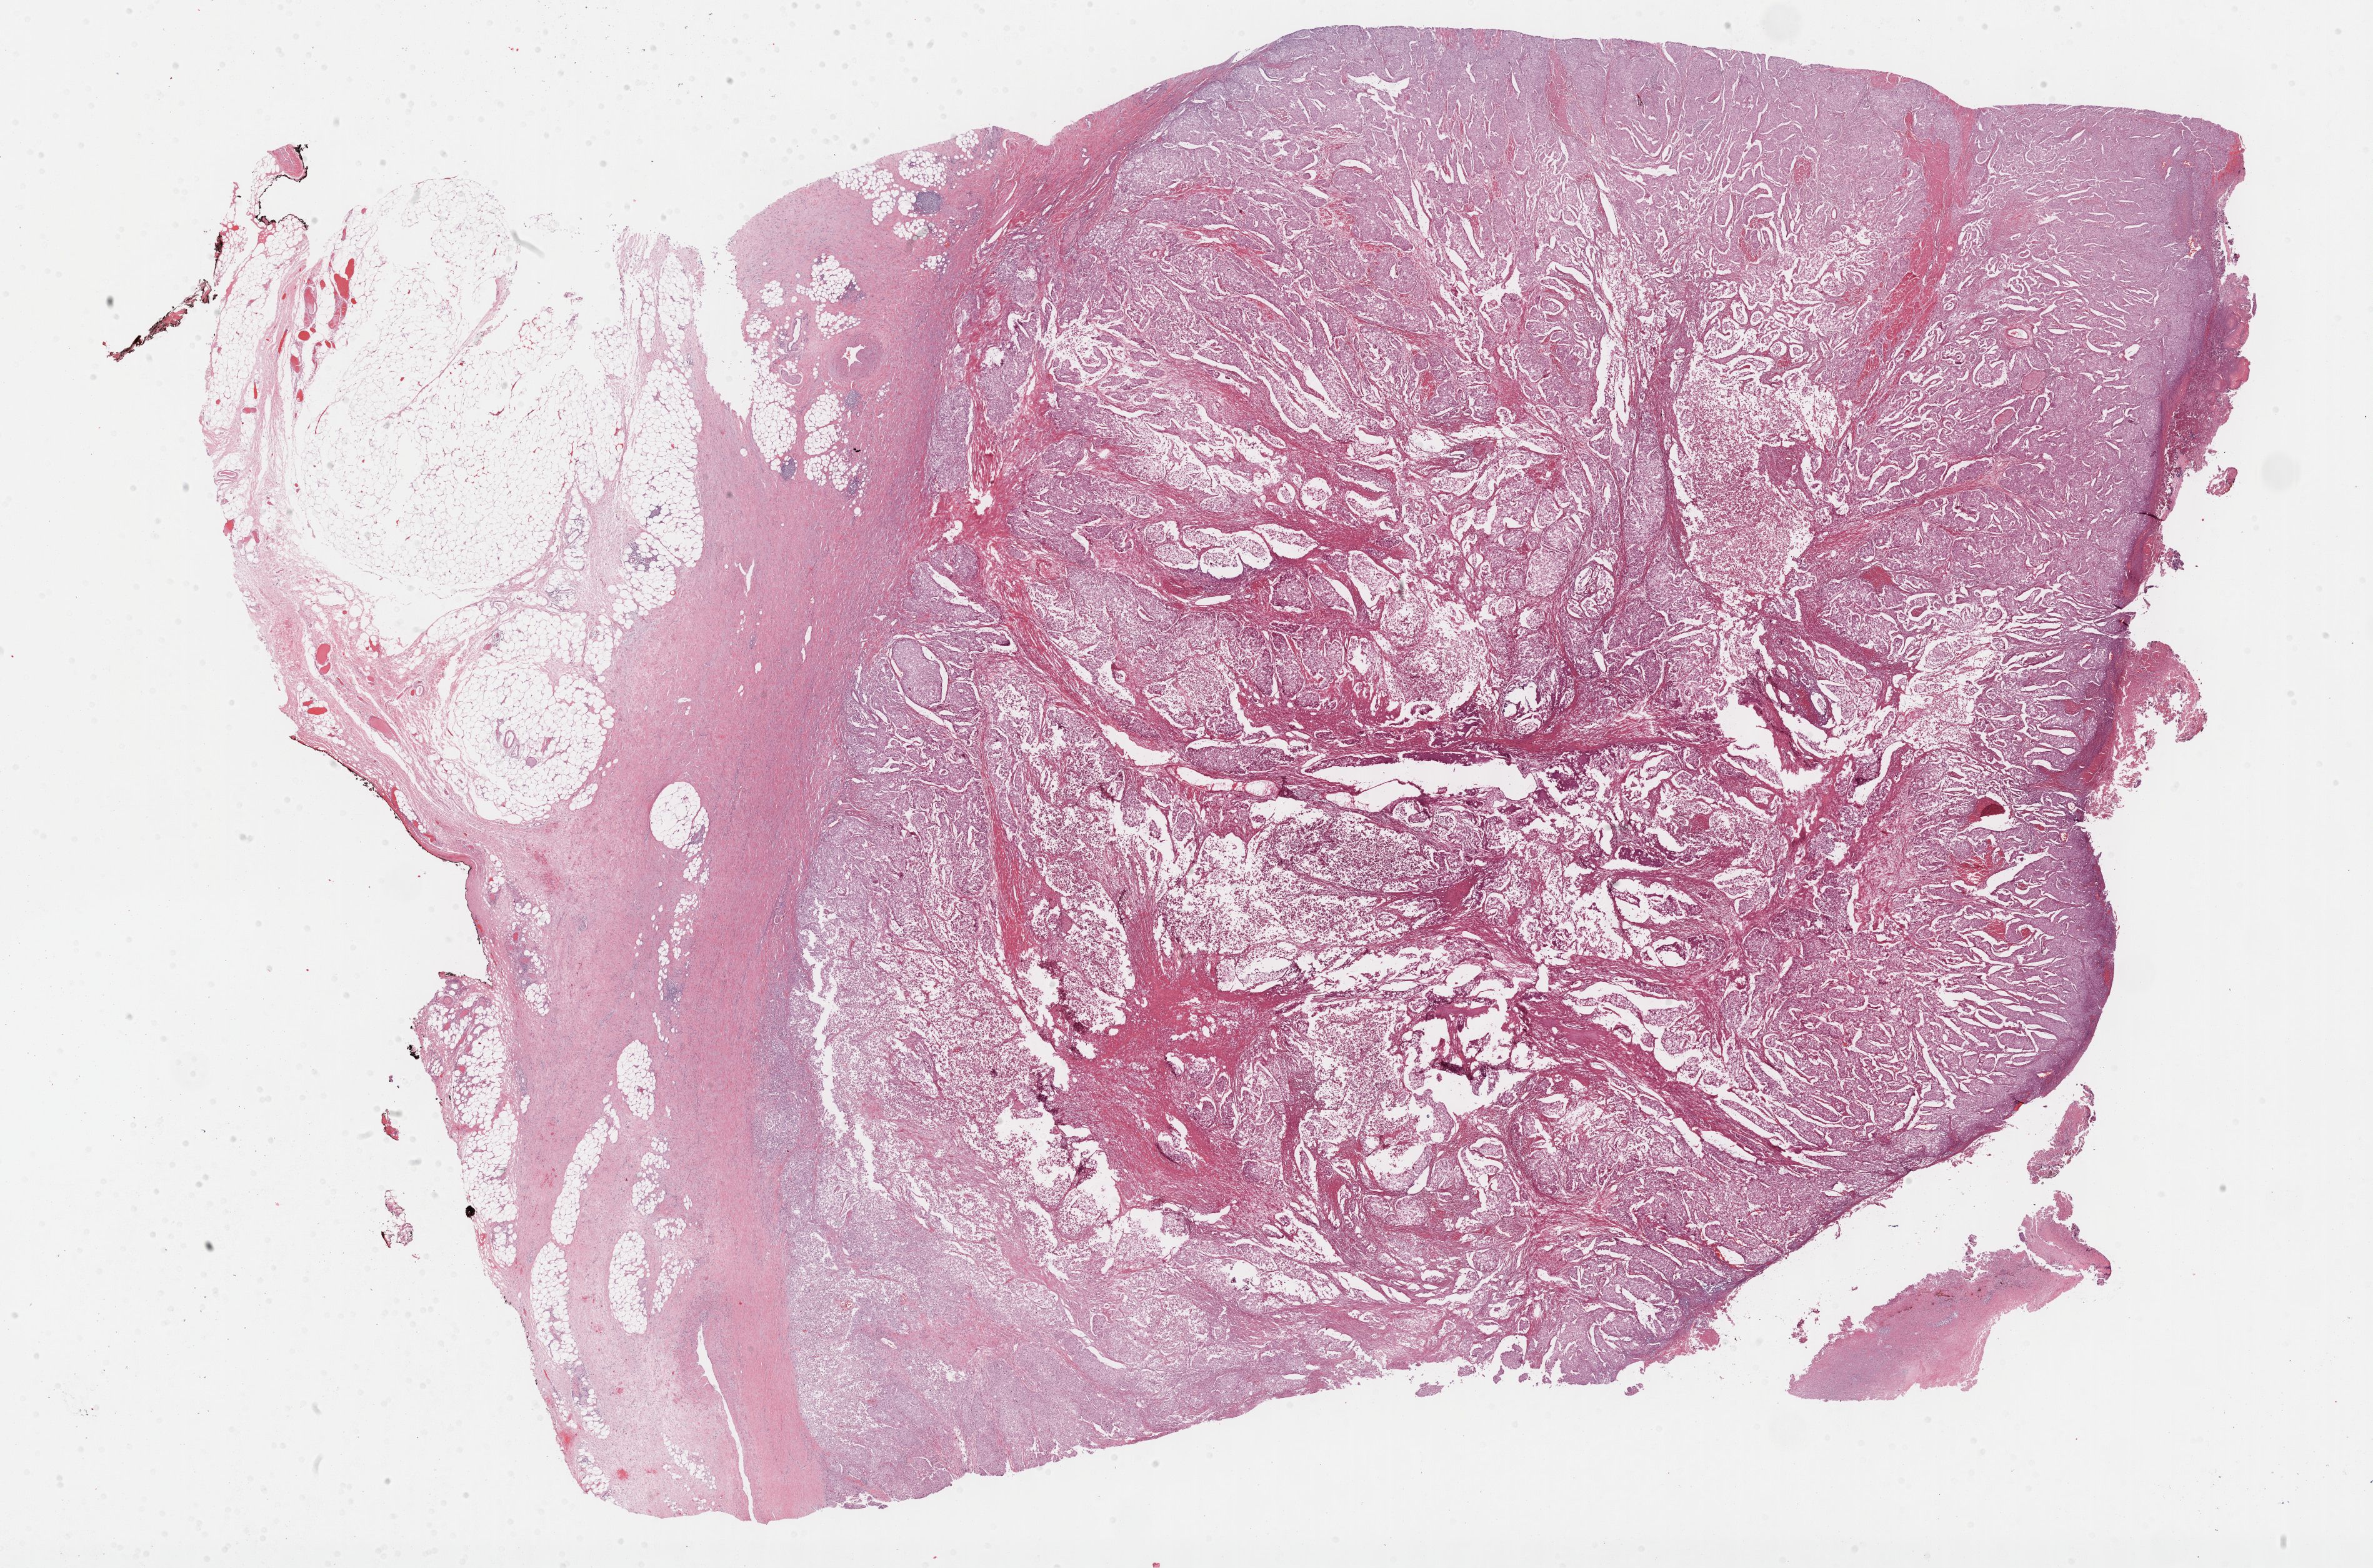
Digitized H&E-stained tissue section (whole slide) — shown as a low-resolution overview of the whole scanned area (about 30.7 x 20.3 mm, from a 40x scan). Formalin-fixed paraffin-embedded (FFPE) diagnostic section. Sample: primary tumour, bladder. Patient: male, age at initial diagnosis 79 years.
Pathologic diagnosis: Transitional cell carcinoma.